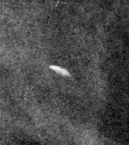
Cropped region of a digitized screen-film mammogram centred on a radiologist-marked abnormality; left breast; MLO view.
Calcifications, distribution regional; BI-RADS assessment category 2; subtlety rating 3 on a 1 (subtle) to 5 (obvious) scale; benign without callback (not worked up further).